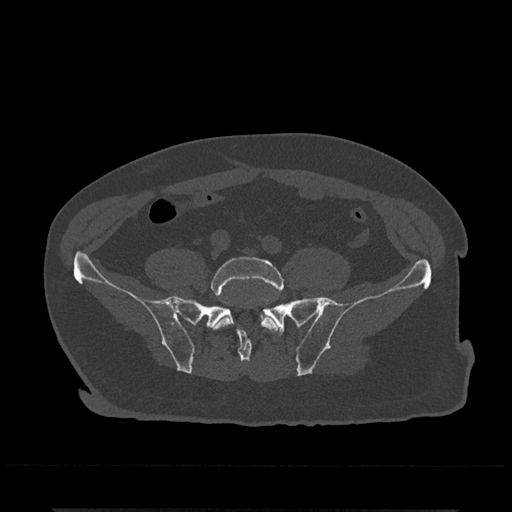
CT including the spine, one axial slice. Slice 55 of 797 in the series (ordered by position). Reconstruction kernel Br40s/3. Bone window (W 1800 / L 400 HU). 0.5 mm slice thickness. 512 × 512 image matrix. Male patient, age 67 years. From the clinical record (not read from this slice): primary cancer: prostate.
Annotated regions visible in this slice (semi-automatically segmented with operator editing):
- L5 vertebra: box from (x=210, y=256) to (x=284, y=332) px